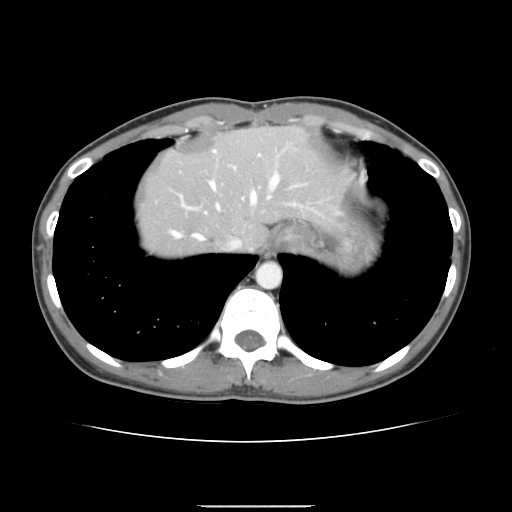
Contrast-enhanced abdominal CT, one axial slice. Intravenous contrast given. Soft-tissue window (W 400 / L 40 HU). 512 × 512 image matrix. Female patient, age 32 years. From the clinical record (not read from this slice): diagnosis: colorectal cancer liver metastases, imaged before liver resection; multiple liver metastases: yes; largest metastasis: 0.7 cm; chemotherapy before resection: yes.
Outlined on this slice (outlined manually by an expert reader):
- hepatic veins: bounding box [x1, y1, x2, y2] px = [171, 172, 279, 250]
- liver: [139, 127, 348, 257]
- planned liver remnant (the part of the liver to remain after resection): [140, 128, 348, 251]
- portal vein (with intrahepatic branches): [182, 150, 297, 213]